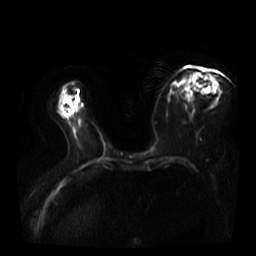
Breast MRI, one axial slice. Position 20 of 40 along the scan axis. Diffusion-weighted series; image 2 of 4 stored at this slice position (different b-values; order by instance number). 3 T. 5 mm slice thickness. 256 × 256 image matrix, field of view 360 × 360 mm. Female patient.
Structures marked on this image (expert manual segmentation):
- tumour on diffusion-weighted imaging: bounding box (x1, y1, x2, y2) in pixels: (208, 75, 217, 85)